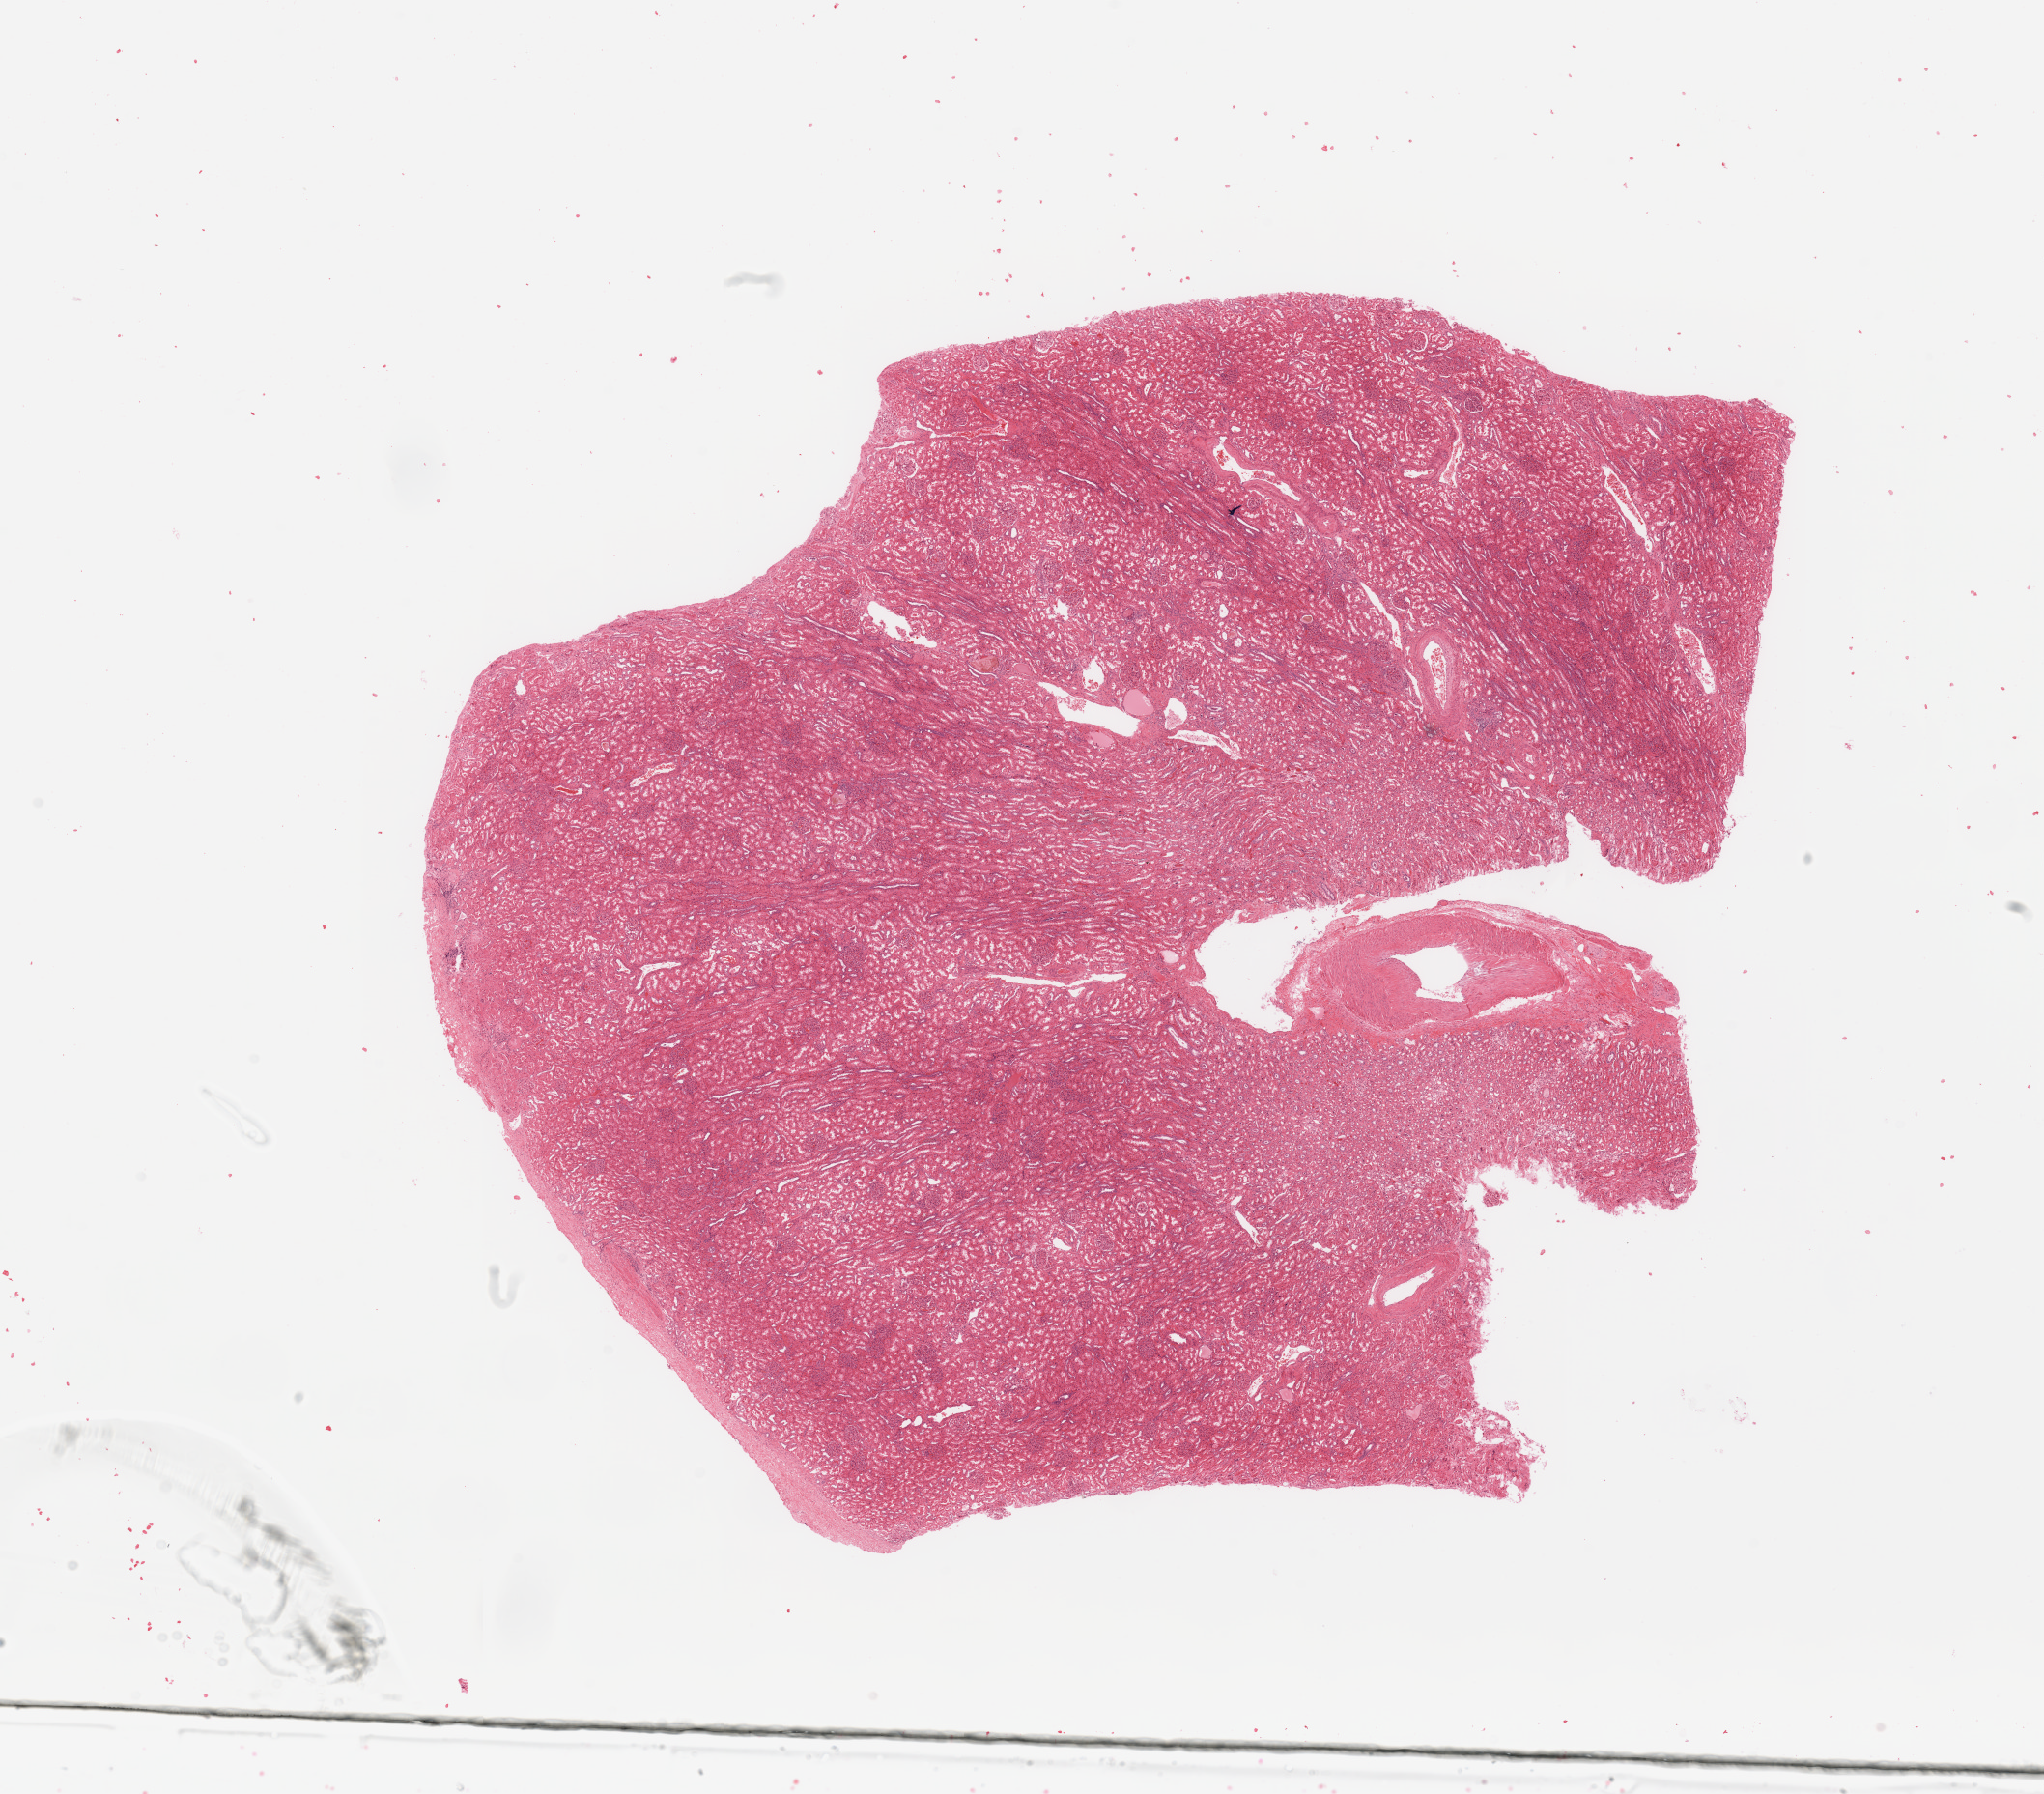
Whole-slide histology image, H&E-stained, a low-resolution overview of the entire scanned area, about 16.7 x 14.7 mm, normal (non-tumour) tissue sample, sampled site: kidney. 61-year-old male patient.
This section: normal (non-tumour) tissue from the same patient. Patient diagnosis: Renal cell carcinoma, NOS.